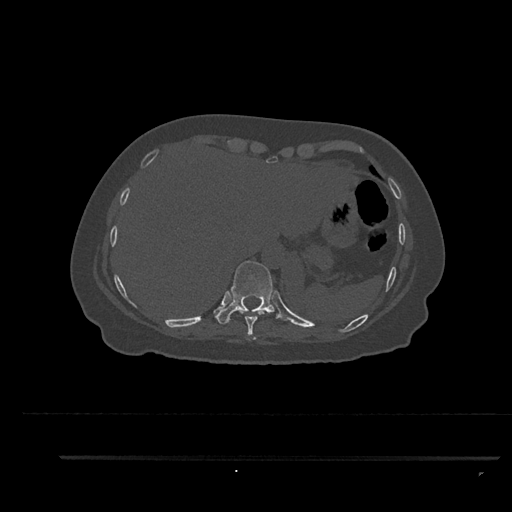
CT including the spine, one axial slice. Slice 384 of 797 in the series (ordered by position). Reconstruction kernel Br40s/3. Bone window (W 1800 / L 400 HU). 0.5 mm slice thickness. 512 × 512 image matrix. Female patient, age 44 years. From the clinical record (not read from this slice): primary cancer: renal.
Structures marked on this image (semi-automatic segmentation, software-assisted and operator-edited):
- T10 vertebra: box from (x=215, y=260) to (x=283, y=324) px
- T9 vertebra: (x=238, y=308)–(x=265, y=341)